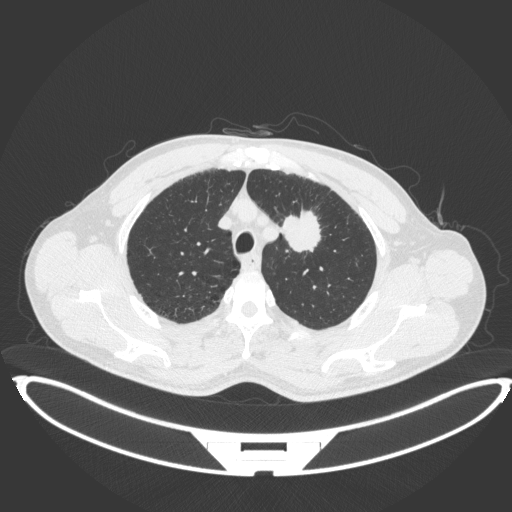
Chest CT, one axial slice. Slice 349 of 407 in the series (ordered by position). Reconstruction kernel B31f. 120 kVp. Lung window (W 1500 / L -600 HU). 1 mm slice thickness. 512 × 512 image matrix. Male patient, age 60 years. From the clinical record (not read from this slice): clinical TNM (as recorded): T2a N0 M0.
Outlined on this slice (bounding box drawn by a radiologist):
- lung tumour (recorded histology: squamous cell carcinoma): bounding box [x1, y1, x2, y2] px = [279, 209, 324, 254]